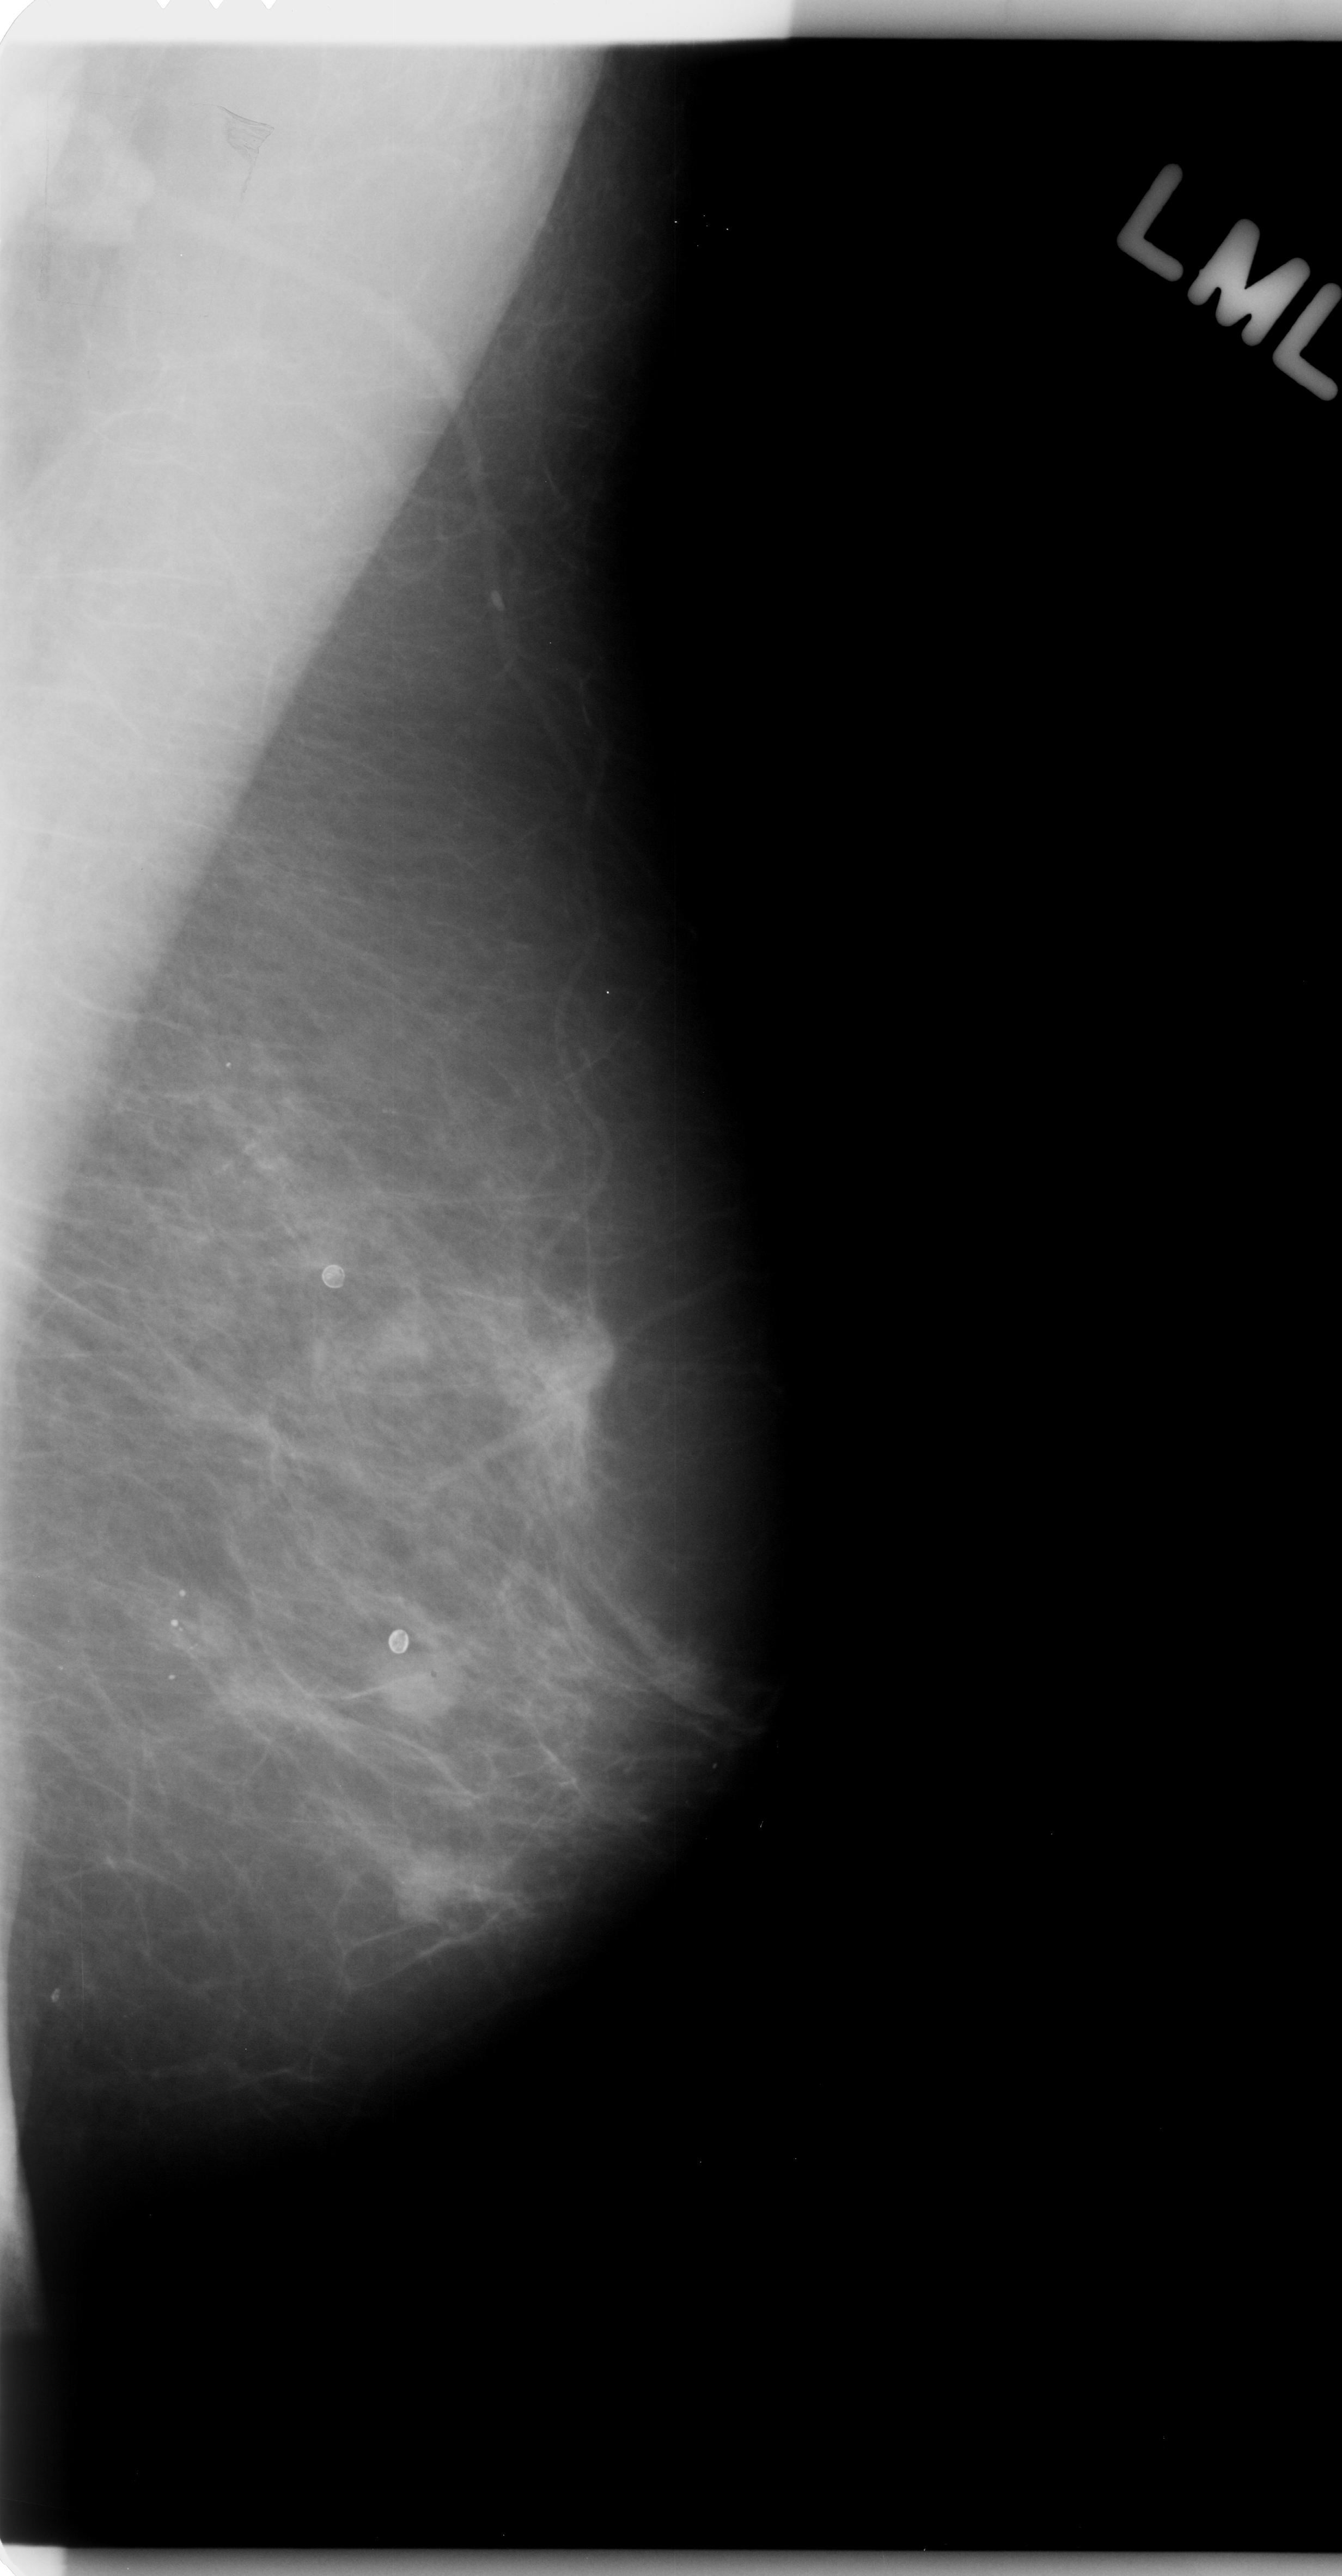
Mammogram (digitized film); left breast; mediolateral oblique (MLO) view; BI-RADS breast density category 1 (scale 1–4); 1342 × 2576 image matrix.
Expert-marked regions of interest on this image (one box per marked abnormality):
- Finding 1 of 3: mass, shape oval, margins microlobulated; BI-RADS assessment category 4; subtlety rating 5 on a 1 (subtle) to 5 (obvious) scale; pathology result (as recorded, not read from the image): malignant: bounding box [x1, y1, x2, y2] px = [357, 1629, 462, 1726]
- Finding 2 of 3: mass, shape oval, margins microlobulated; BI-RADS assessment category 4; subtlety rating 5 on a 1 (subtle) to 5 (obvious) scale; pathology (as recorded): malignant: [393, 1848, 484, 1923]
- Finding 3 of 3: mass, shape oval, margins microlobulated; BI-RADS assessment category 4; subtlety rating 5 on a 1 (subtle) to 5 (obvious) scale; pathology result (as recorded, not read from the image): malignant: [515, 1335, 616, 1442]